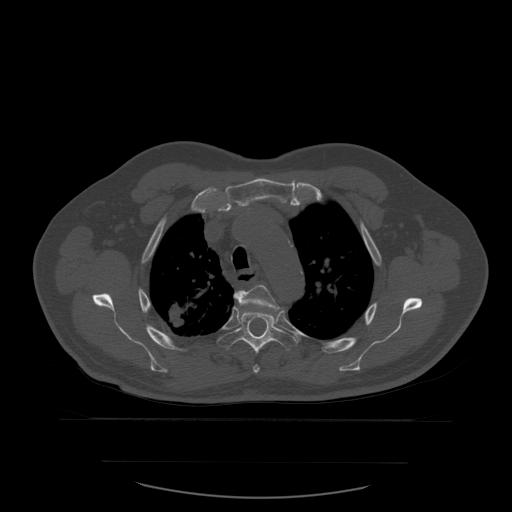
CT including the spine, one axial slice. Slice 430 of 590 in the series (ordered by position). Bone window (W 1800 / L 400 HU). 1.25 mm slice thickness. 512 × 512 image matrix. Patient age 71 years. Case-level facts recorded for this patient, not image findings: primary cancer: lung; vertebrae with lytic lesions (as recorded): T1, T2, L5, S1.
Structures marked on this image (semi-automatically segmented with operator editing):
- T4 vertebra: box from (x=234, y=285) to (x=280, y=374) px
- T5 vertebra: (x=217, y=295)–(x=298, y=355)